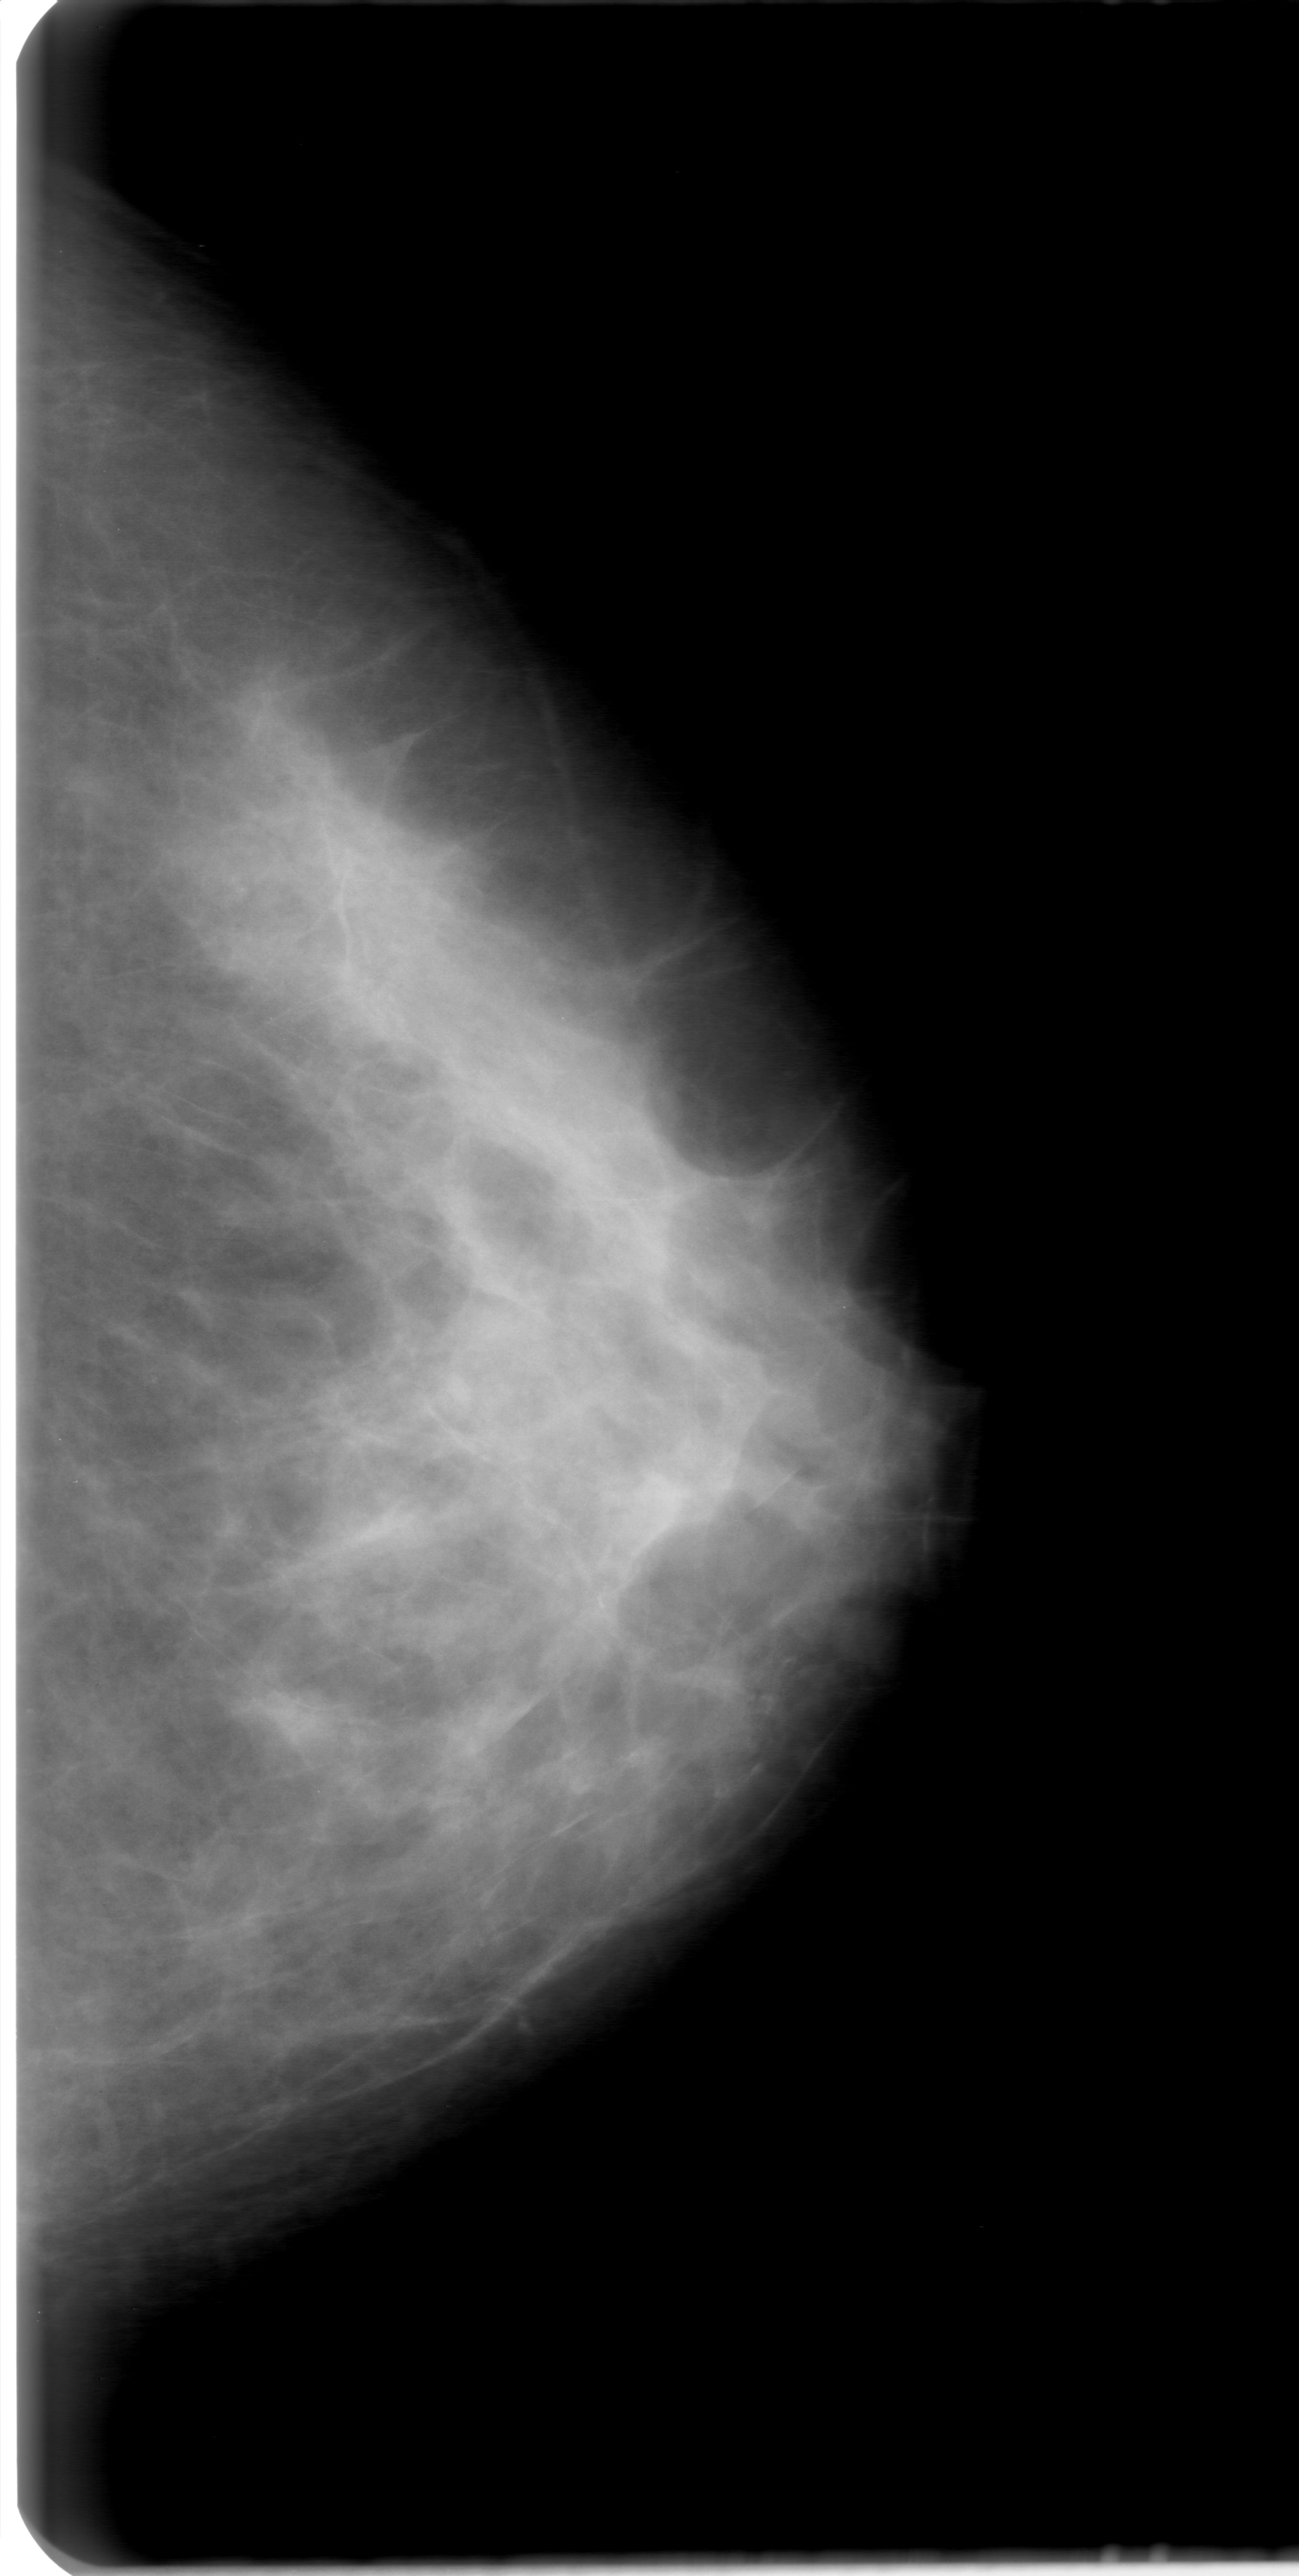
Scanned film-screen mammogram, left breast, CC view, BI-RADS breast density category 3 (scale 1–4).
Radiologist-marked abnormalities on this image: calcifications, morphology amorphous, distribution segmental; BI-RADS assessment category 0 (incomplete: needs additional imaging); pathology result (as recorded, not read from the image): benign.